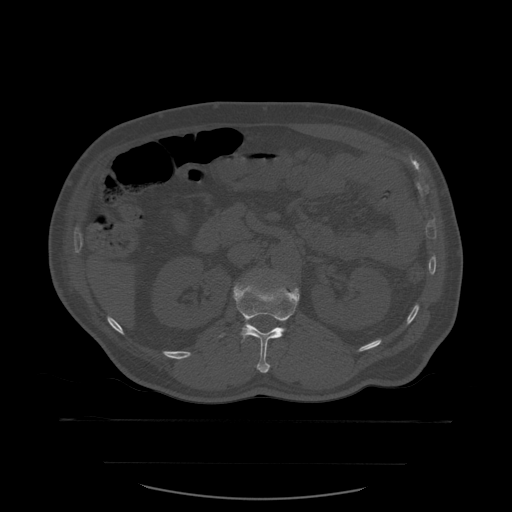
CT including the spine, one axial slice; slice 243 of 590 in the series (ordered by position); bone window (W 1800 / L 400 HU); 1.25 mm slice thickness; 512 × 512 image matrix, field of view 479 × 479 mm. Patient age 71 years. Case-level facts recorded for this patient, not image findings: primary cancer: lung; vertebrae with lytic lesions (as recorded): T1, T2, L5, S1.
Annotated regions visible in this slice (semi-automatic segmentation, software-assisted and operator-edited):
- L1 vertebra: bounding box <218,277,300,373> (left, top, right, bottom; pixels)
- L2 vertebra: <235,283,248,288>